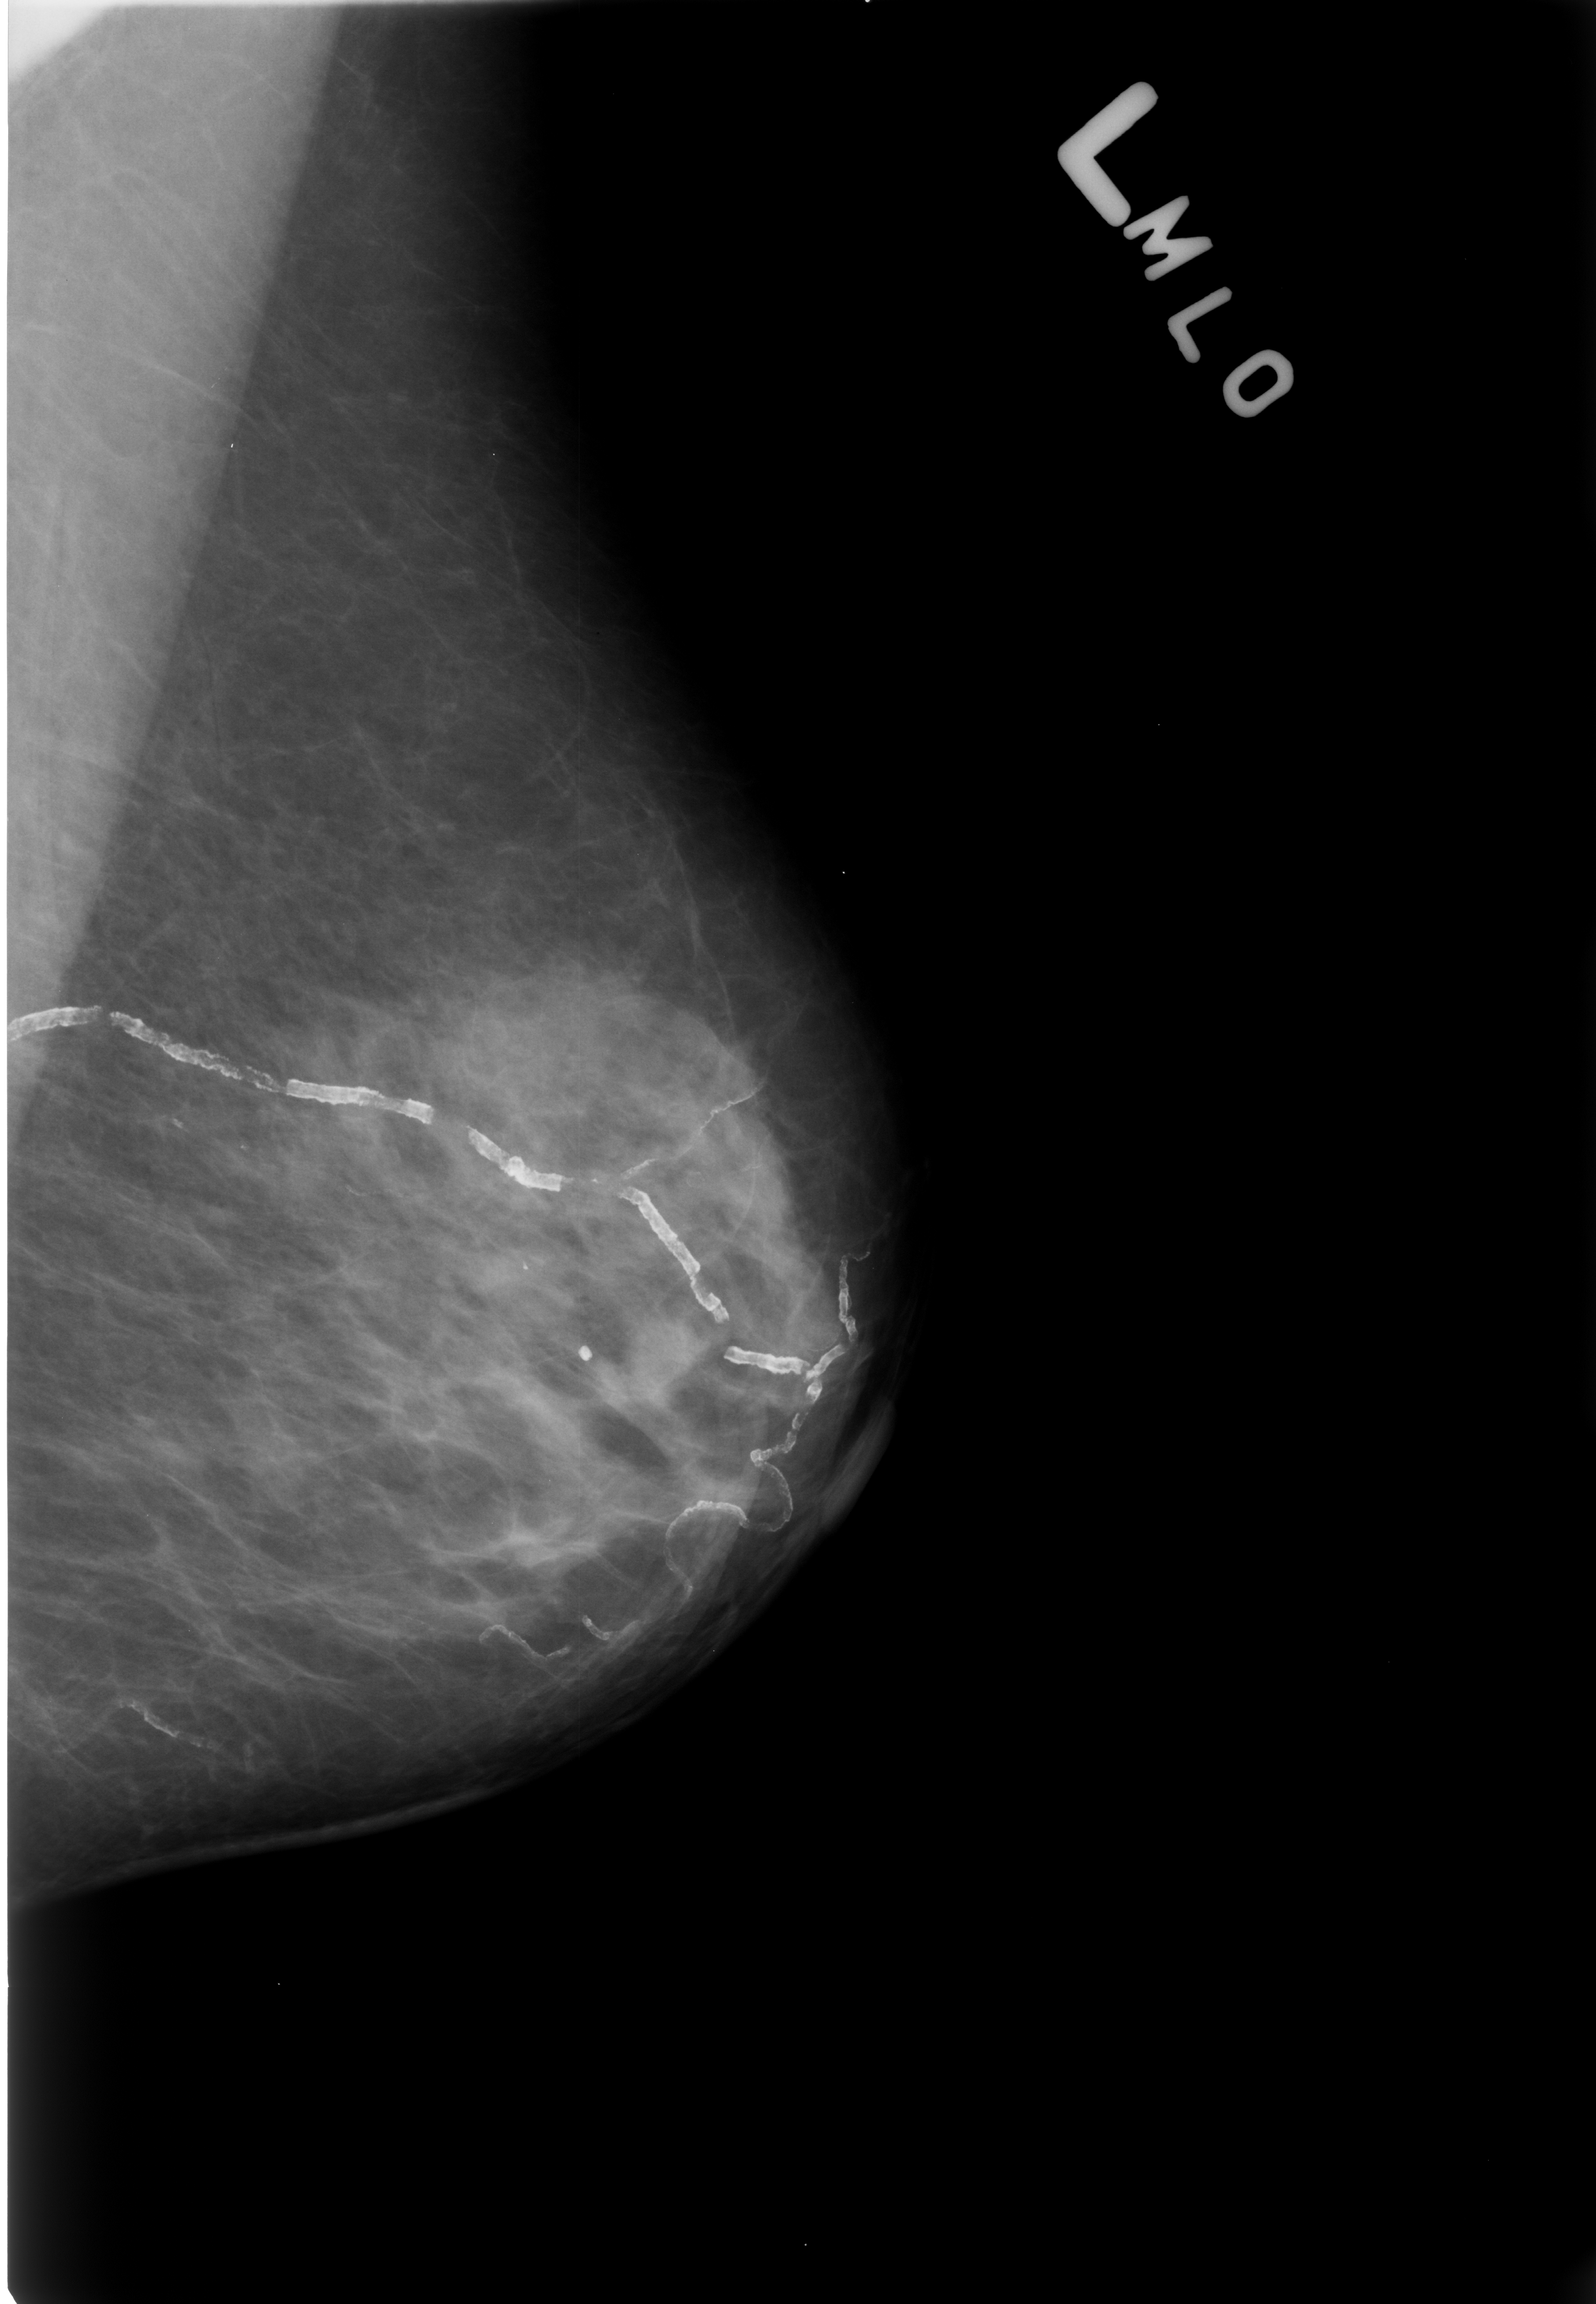
Mammogram (digitized film), left breast, MLO view, breast composition: scattered fibroglandular densities (BI-RADS density category 2 of 4).
Marked findings (only marked abnormalities are described; nothing is implied about the rest of the image): calcifications, morphology vascular; BI-RADS assessment category 2; benign without callback (not worked up further).